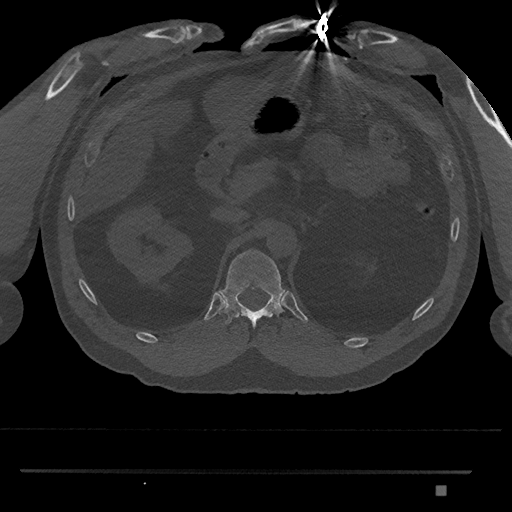
CT including the spine, one axial slice; position 888 of 1134 along the scan axis; reconstruction kernel Br40s/3; bone window (W 1800 / L 400 HU); 0.5 mm slice thickness; 512 × 512 image matrix. Patient: male, 65 years. From the clinical record (not read from this slice): primary cancer: prostate.
Outlined on this slice (semi-automatic segmentation, software-assisted and operator-edited):
- T12 vertebra: bounding box [x1, y1, x2, y2] px = [219, 249, 286, 329]